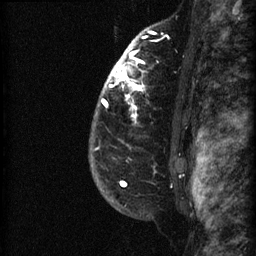
Breast MRI (dynamic contrast-enhanced), one sagittal slice. Slice 54 of 60 in the series (ordered by position). Dynamic contrast-enhanced series, image 2 of 3 at this slice position (ordered by acquisition). 1.5 T. TE 4.2 ms, TR 22.7 ms. 1.5 mm slice thickness. 256 × 256 image matrix, field of view 180 × 180 mm. Patient: female, 48 years. Case-level facts recorded for this patient, not image findings: setting: breast cancer imaged before/during neoadjuvant chemotherapy; receptor status: triple-negative.
Annotated regions visible in this slice (semi-automatic segmentation, software-assisted and operator-edited):
- analysis volume of interest (the breast-tissue region the enhancement analysis was run in; not a lesion): box from (x=89, y=27) to (x=191, y=180) px
- tumour enhancement mask (voxels above the 90 % enhancement threshold inside the analysis volume of interest): (x=101, y=32)–(x=156, y=116)